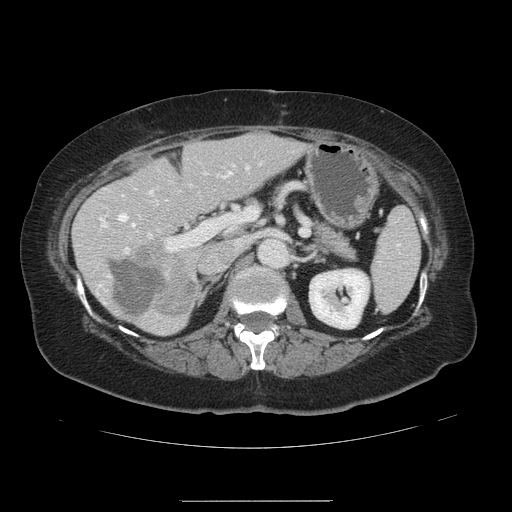
Contrast-enhanced abdominal CT, one axial slice; position 69 of 141 along the scan axis; 120 kVp; intravenous contrast given; soft-tissue window (W 400 / L 40 HU); 2.5 mm slice thickness; 512 × 512 image matrix. Female patient, age 74 years. Case-level facts recorded for this patient, not image findings: diagnosis: colorectal cancer liver metastases, imaged before liver resection; multiple liver metastases: yes; largest metastasis: 7 cm; disease in both lobes: yes.
Outlined on this slice (expert manual segmentation):
- hepatic veins: bounding box <118,189,158,228> (left, top, right, bottom; pixels)
- liver: <74,134,302,334>
- planned liver remnant (the part of the liver to remain after resection): <78,134,302,334>
- portal vein (with intrahepatic branches): <99,164,248,253>
- liver metastasis: <109,261,165,316>
- liver metastasis: <134,243,194,316>